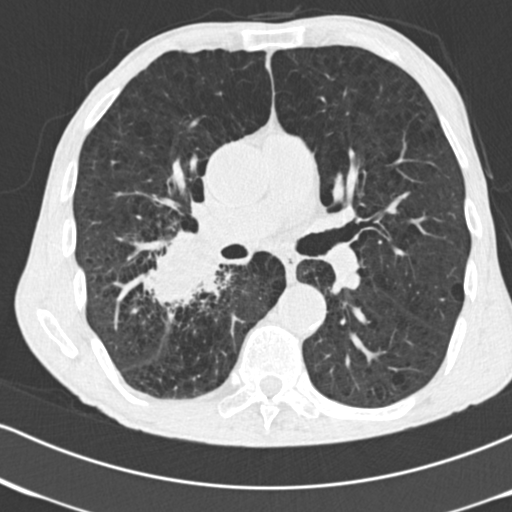
Low-dose screening chest CT, axial slice, second annual screen, lung window (W 1500 / L -600 HU), slice 88 of 182 in the series, 512 × 512 image matrix. Male, age 64 years at enrolment. Current smoker at enrolment.
Lesion marked by an expert reader, bounding box [x1, y1, x2, y2] px = [132, 231, 238, 328]. Screening reader's record for this exam (one nodule recorded; not confirmed to be the boxed lesion): non-calcified nodule or mass ≥4 mm, 52 × 37 mm, spiculated (stellate) margins, soft tissue attenuation, pre-existing on the prior screen: no. Later outcome: lung cancer diagnosed 28 days after this screen — adenocarcinoma, NOS, right lower lobe, stage IV (AJCC 6th edition), 60 mm at pathology.